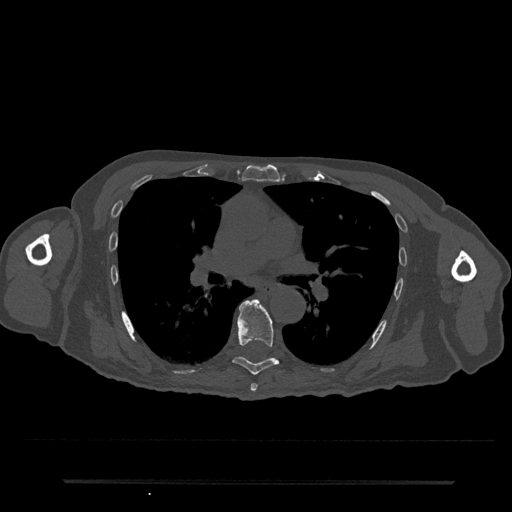
CT including the spine, one axial slice; position 478 of 797 along the scan axis; reconstruction kernel Br40s/3; 120 kVp; bone window (W 1800 / L 400 HU); 512 × 512 image matrix, field of view 427 × 427 mm. Male patient, age 74 years. From the clinical record (not read from this slice): primary cancer: prostate.
Annotated regions visible in this slice (semi-automatically segmented with operator editing):
- T6 vertebra: box from (x=250, y=383) to (x=257, y=392) px
- T7 vertebra: (x=233, y=299)–(x=279, y=375)